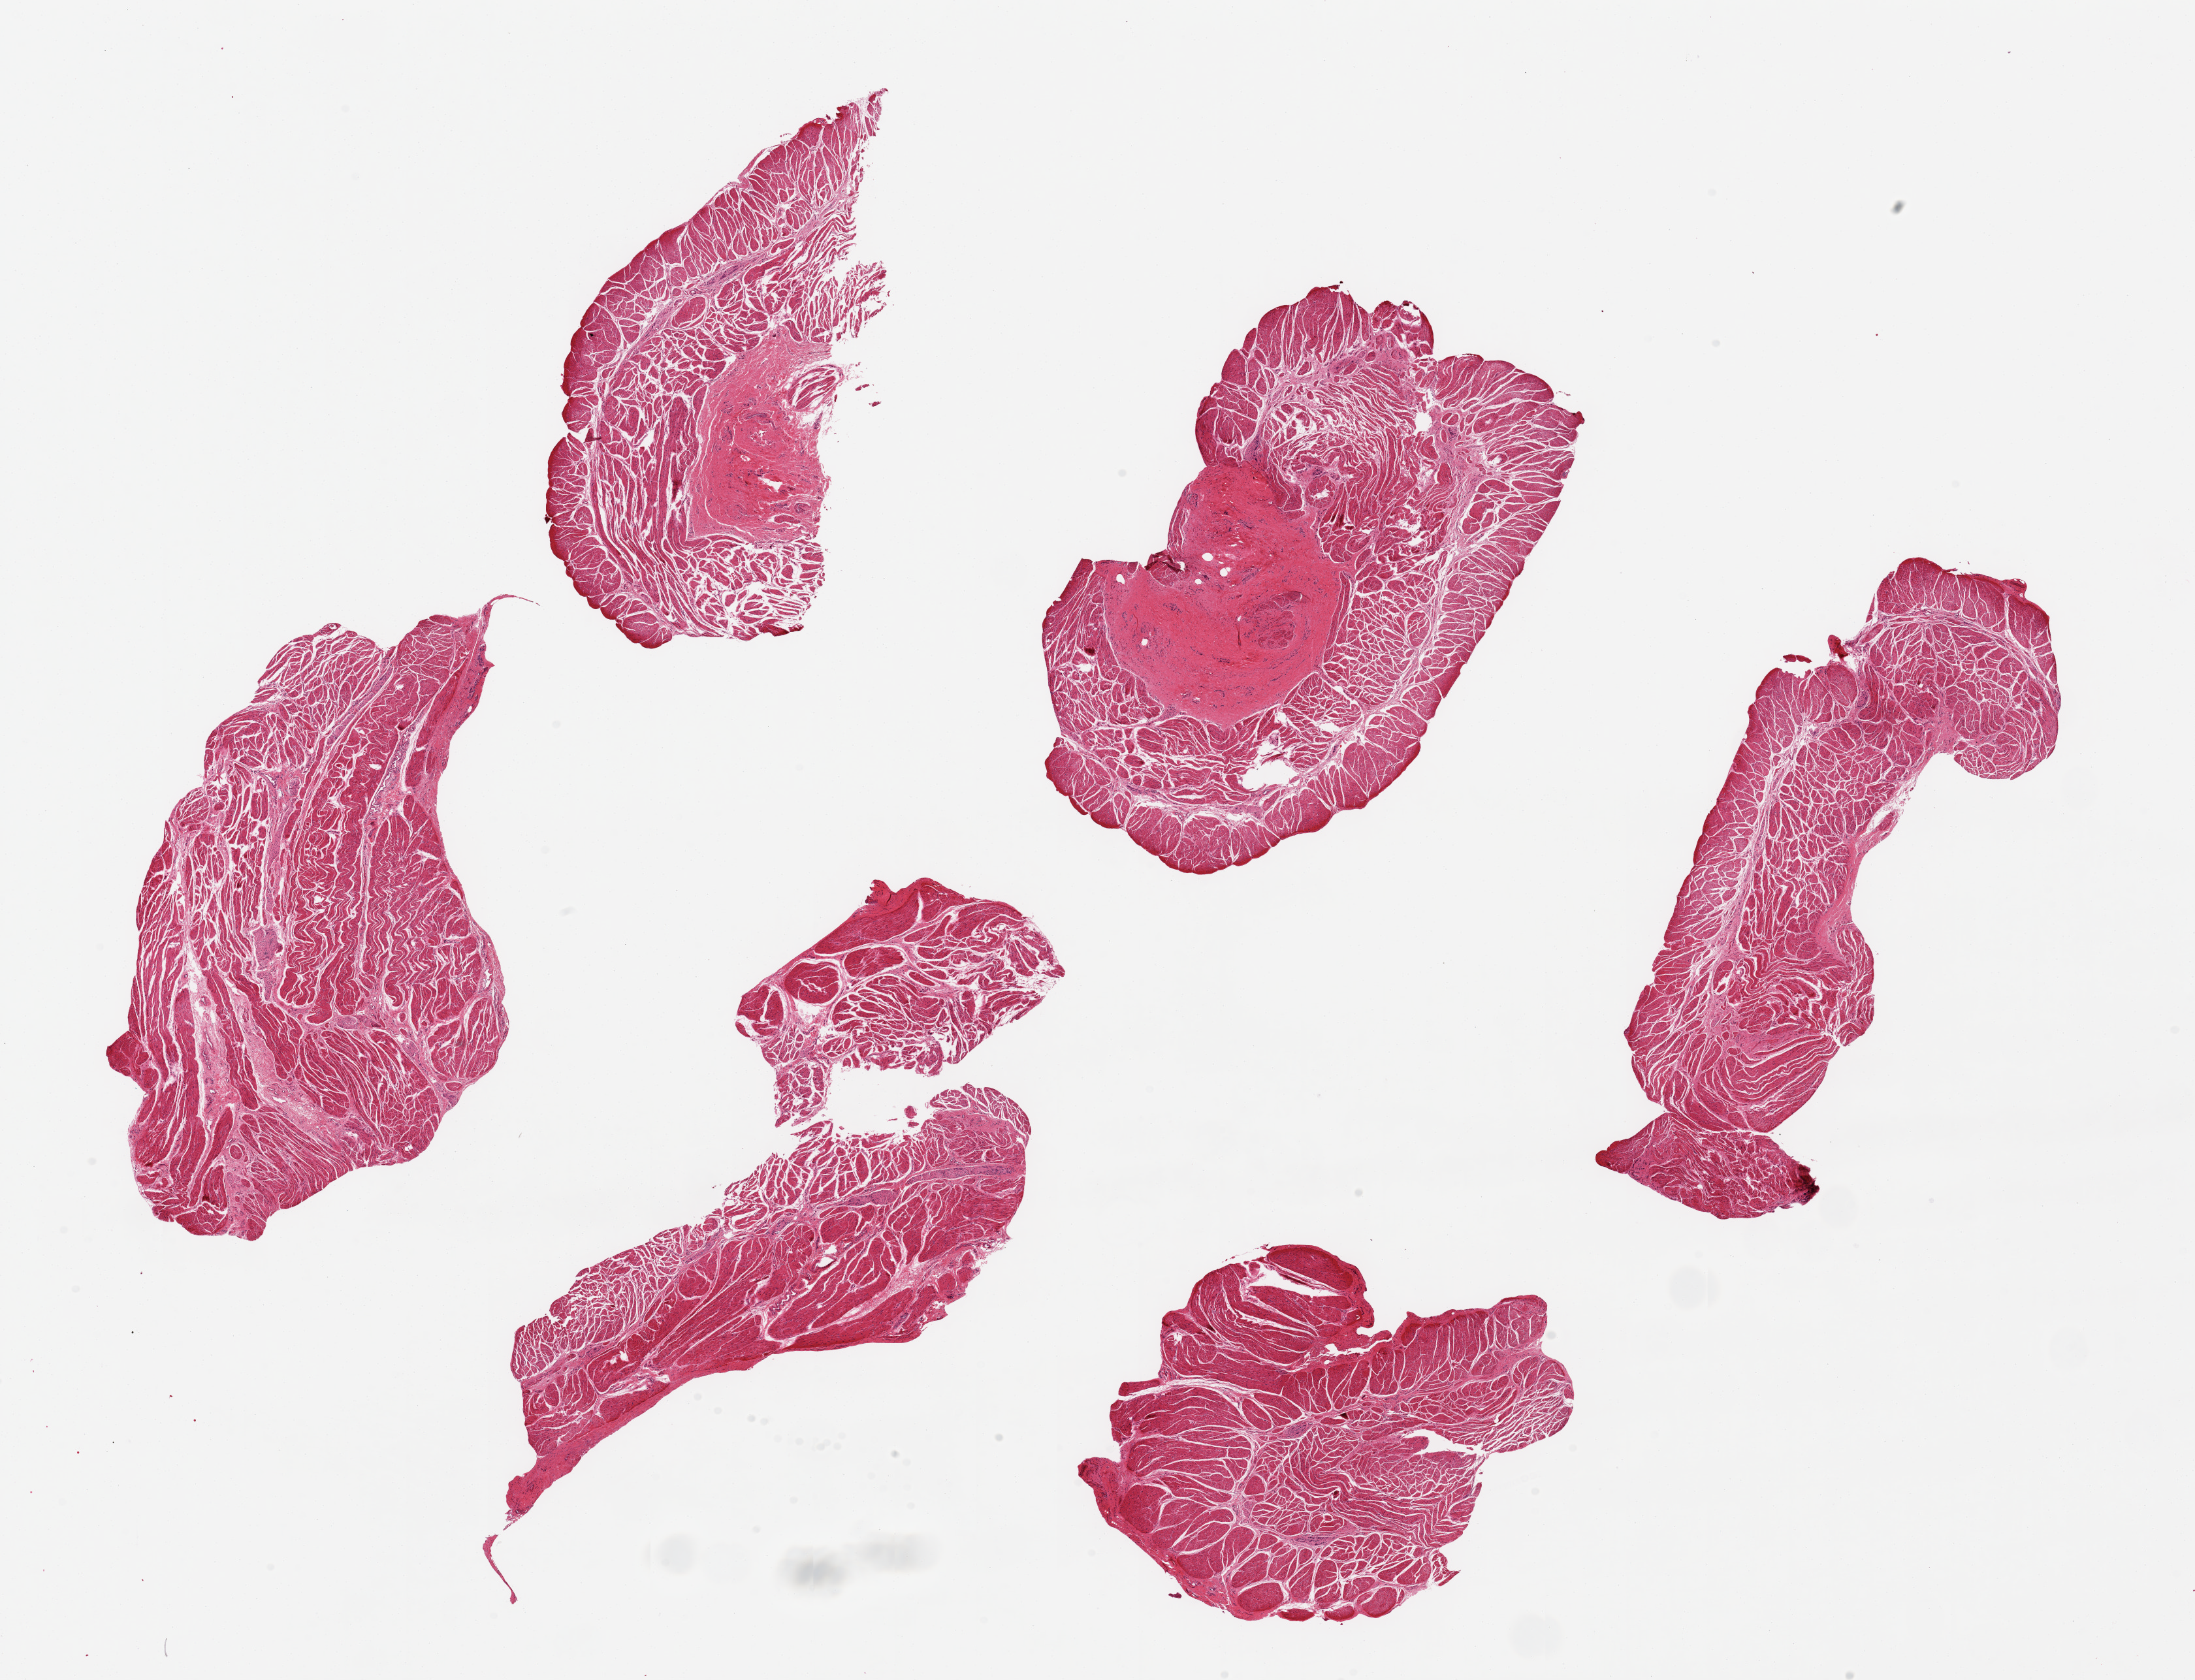
Haematoxylin and eosin whole-slide image — whole scanned area (about 26.6 x 20.3 mm) shown as a low-resolution overview. PAXgene-fixed, paraffin-embedded tissue. Section of esophageal muscle (target tissue). Tissue donor sample. Donor: female.
Pathologist's review note for this sample: 6 pieces up to 7x4 mm; 1 has a 2.8 mm circular focus of fibrotic submucosa.